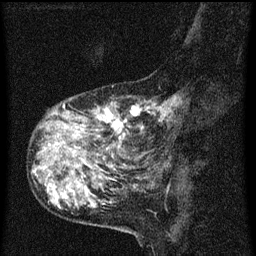
Breast MRI (dynamic contrast-enhanced), one sagittal slice. Position 16 of 60 along the scan axis. Dynamic contrast-enhanced series, image 2 of 3 at this slice position (ordered by acquisition). 1.5 T. TE 4.2 ms, TR 8 ms. 2 mm slice thickness. 256 × 256 image matrix. Female patient, age 55 years.
Structures marked on this image (semi-automatically segmented with operator editing):
- analysis volume of interest (the breast-tissue region the enhancement analysis was run in; not a lesion): bounding box <38,94,181,159> (left, top, right, bottom; pixels)
- tumour enhancement mask (voxels above the 70 % enhancement threshold inside the analysis volume of interest): <64,98,177,141>